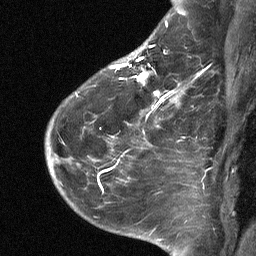
Breast MRI (dynamic contrast-enhanced), one sagittal slice. Dynamic contrast-enhanced study with each time point stored as its own series, time point 2 of 3 at this slice position (early post-contrast, ordered by acquisition time). 1.5 T. TE 4.8 ms, TR 27 ms. 2 mm slice thickness. 256 × 256 image matrix, field of view 180 × 180 mm. Female patient, age 51 years. From the clinical record (not read from this slice): setting: breast cancer imaged before/during neoadjuvant chemotherapy; receptor status: HR-positive, HER2-negative.
Outlined on this slice (semi-automatically segmented with operator editing):
- analysis volume of interest (the breast-tissue region the enhancement analysis was run in; not a lesion): bounding box (x1, y1, x2, y2) in pixels: (72, 34, 182, 118)
- tumour enhancement mask (voxels above the 90 % enhancement threshold inside the analysis volume of interest): (110, 57, 176, 110)